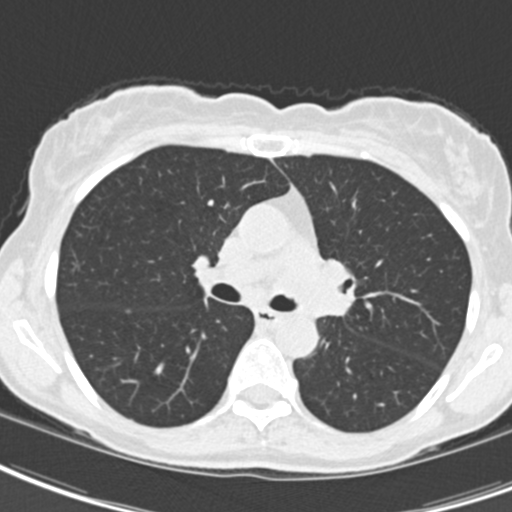
Low-dose screening chest CT, one axial slice. Slice 124 of 189 in the series (ordered by position). Reconstruction kernel B30f. 120 kVp. Lung window (W 1500 / L -600 HU). 512 × 512 image matrix, field of view 279 × 279 mm.
Outlined on this slice (outlined manually by an expert reader):
- lesion 2 (tumor, hilum of left lung): box from (x=284, y=258) to (x=353, y=314) px